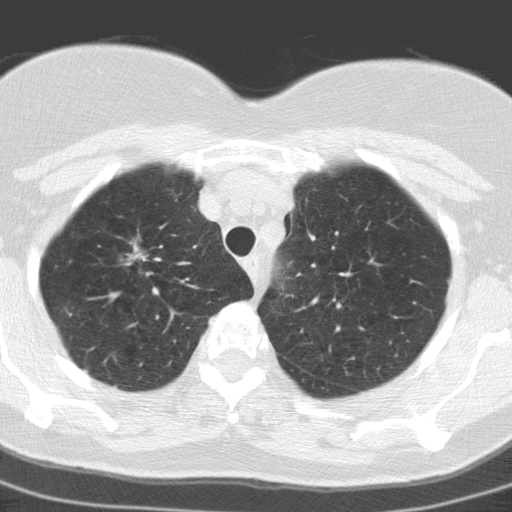
Low-dose screening chest CT, axial slice; first (baseline) screen; lung window (W 1500 / L -600 HU); standard (soft-tissue) reconstruction kernel (C). Female participant, aged 60 years at enrolment. Former smoker at enrolment.
Lesion marked by an expert reader, box from (x=103, y=232) to (x=159, y=279) px. Screening reader's record for this exam: no non-calcified nodule ≥4 mm recorded. Official screen result: negative screen, minor abnormalities not suspicious for lung cancer. Participant outcome: lung cancer diagnosed 447 days after this screen (after the second annual screen) — adenocarcinoma, NOS, right upper lobe, moderately differentiated (G2), stage IA (AJCC 6th edition), 23 mm at pathology.